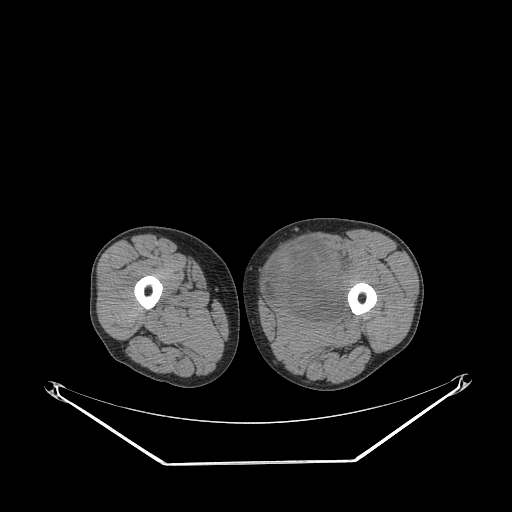
CT of an extremity soft-tissue mass (from a PET/CT study), one axial slice. Slice 239 of 267 in the series (ordered by position). Soft-tissue window (W 400 / L 40 HU). 512 × 512 image matrix. Male patient. Case-level facts recorded for this patient, not image findings: histological type: pleiomorphic liposarcoma; grade: high; site of the primary tumour: left thigh.
Outlined on this slice (expert contour drawn on MRI and transferred to this co-registered scan by the dataset authors):
- gross tumour volume including surrounding oedema: bounding box [x1, y1, x2, y2] px = [265, 238, 353, 321]
- gross tumour volume (mass): [267, 238, 348, 321]